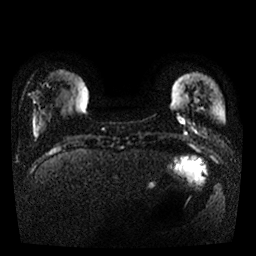
Breast MRI, one axial slice. Position 3 of 25 along the scan axis. Diffusion-weighted series; image 2 of 4 stored at this slice position (different b-values; order by instance number). 1.5 T. 4 mm slice thickness. 256 × 256 image matrix, field of view 330 × 330 mm. Female patient.
Structures marked on this image (expert manual segmentation):
- tumour on diffusion-weighted imaging: bounding box [x1, y1, x2, y2] px = [177, 115, 187, 124]